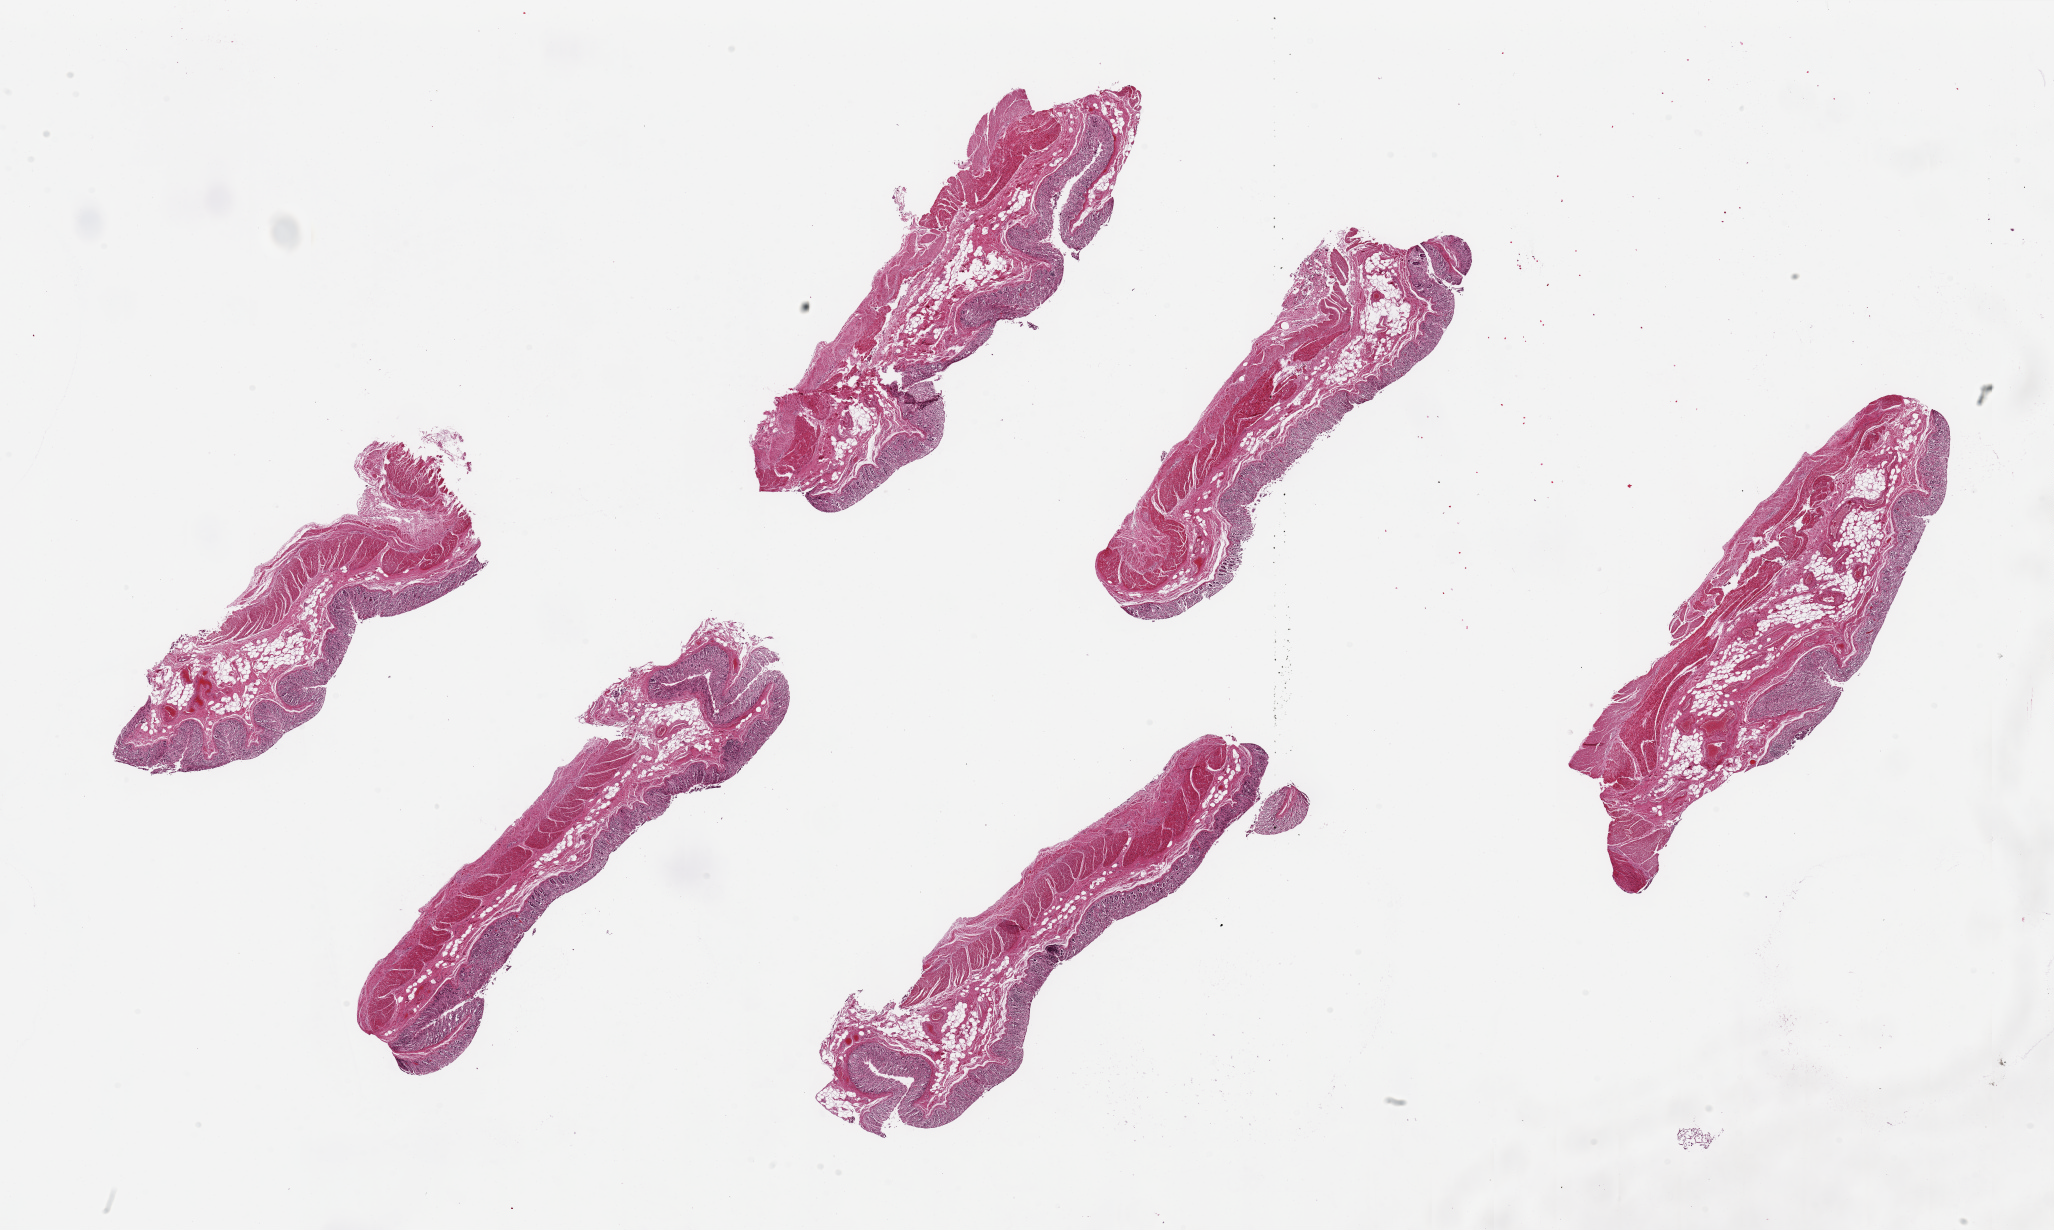
Whole-slide image, haematoxylin and eosin stain — whole scanned area (about 32.5 x 19.5 mm, from a 20x scan) shown as a low-resolution overview. PAXgene-fixed paraffin-embedded (PFPE) section. Sampled site (target tissue): transverse colon. Tissue donor sample. Donor: male.
Review note (as recorded): 6 pieces ~8x2mm, mucosa badly autolyzed.